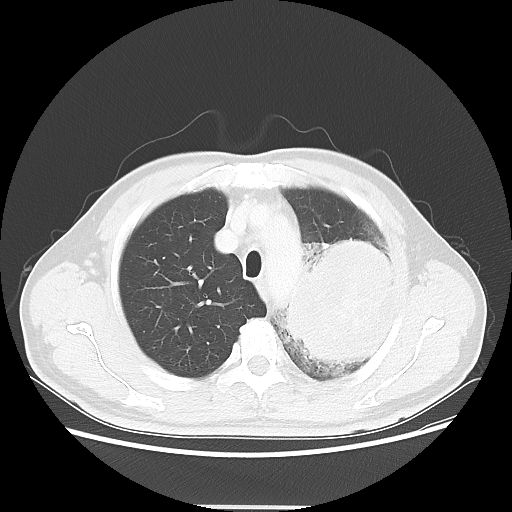
Chest CT, one axial slice; position 43 of 53 along the scan axis; reconstruction kernel LUNG; lung window (W 1500 / L -600 HU); 5 mm slice thickness; 512 × 512 image matrix, field of view 391 × 391 mm. Male patient, age 60 years. From the clinical record (not read from this slice): clinical TNM (as recorded): T4 N1 M1a; histopathological grade: G3.
Structures marked on this image (rectangle marked by the reading radiologist):
- lung tumour (recorded histology: large cell carcinoma): bounding box (x1, y1, x2, y2) in pixels: (278, 234, 398, 368)